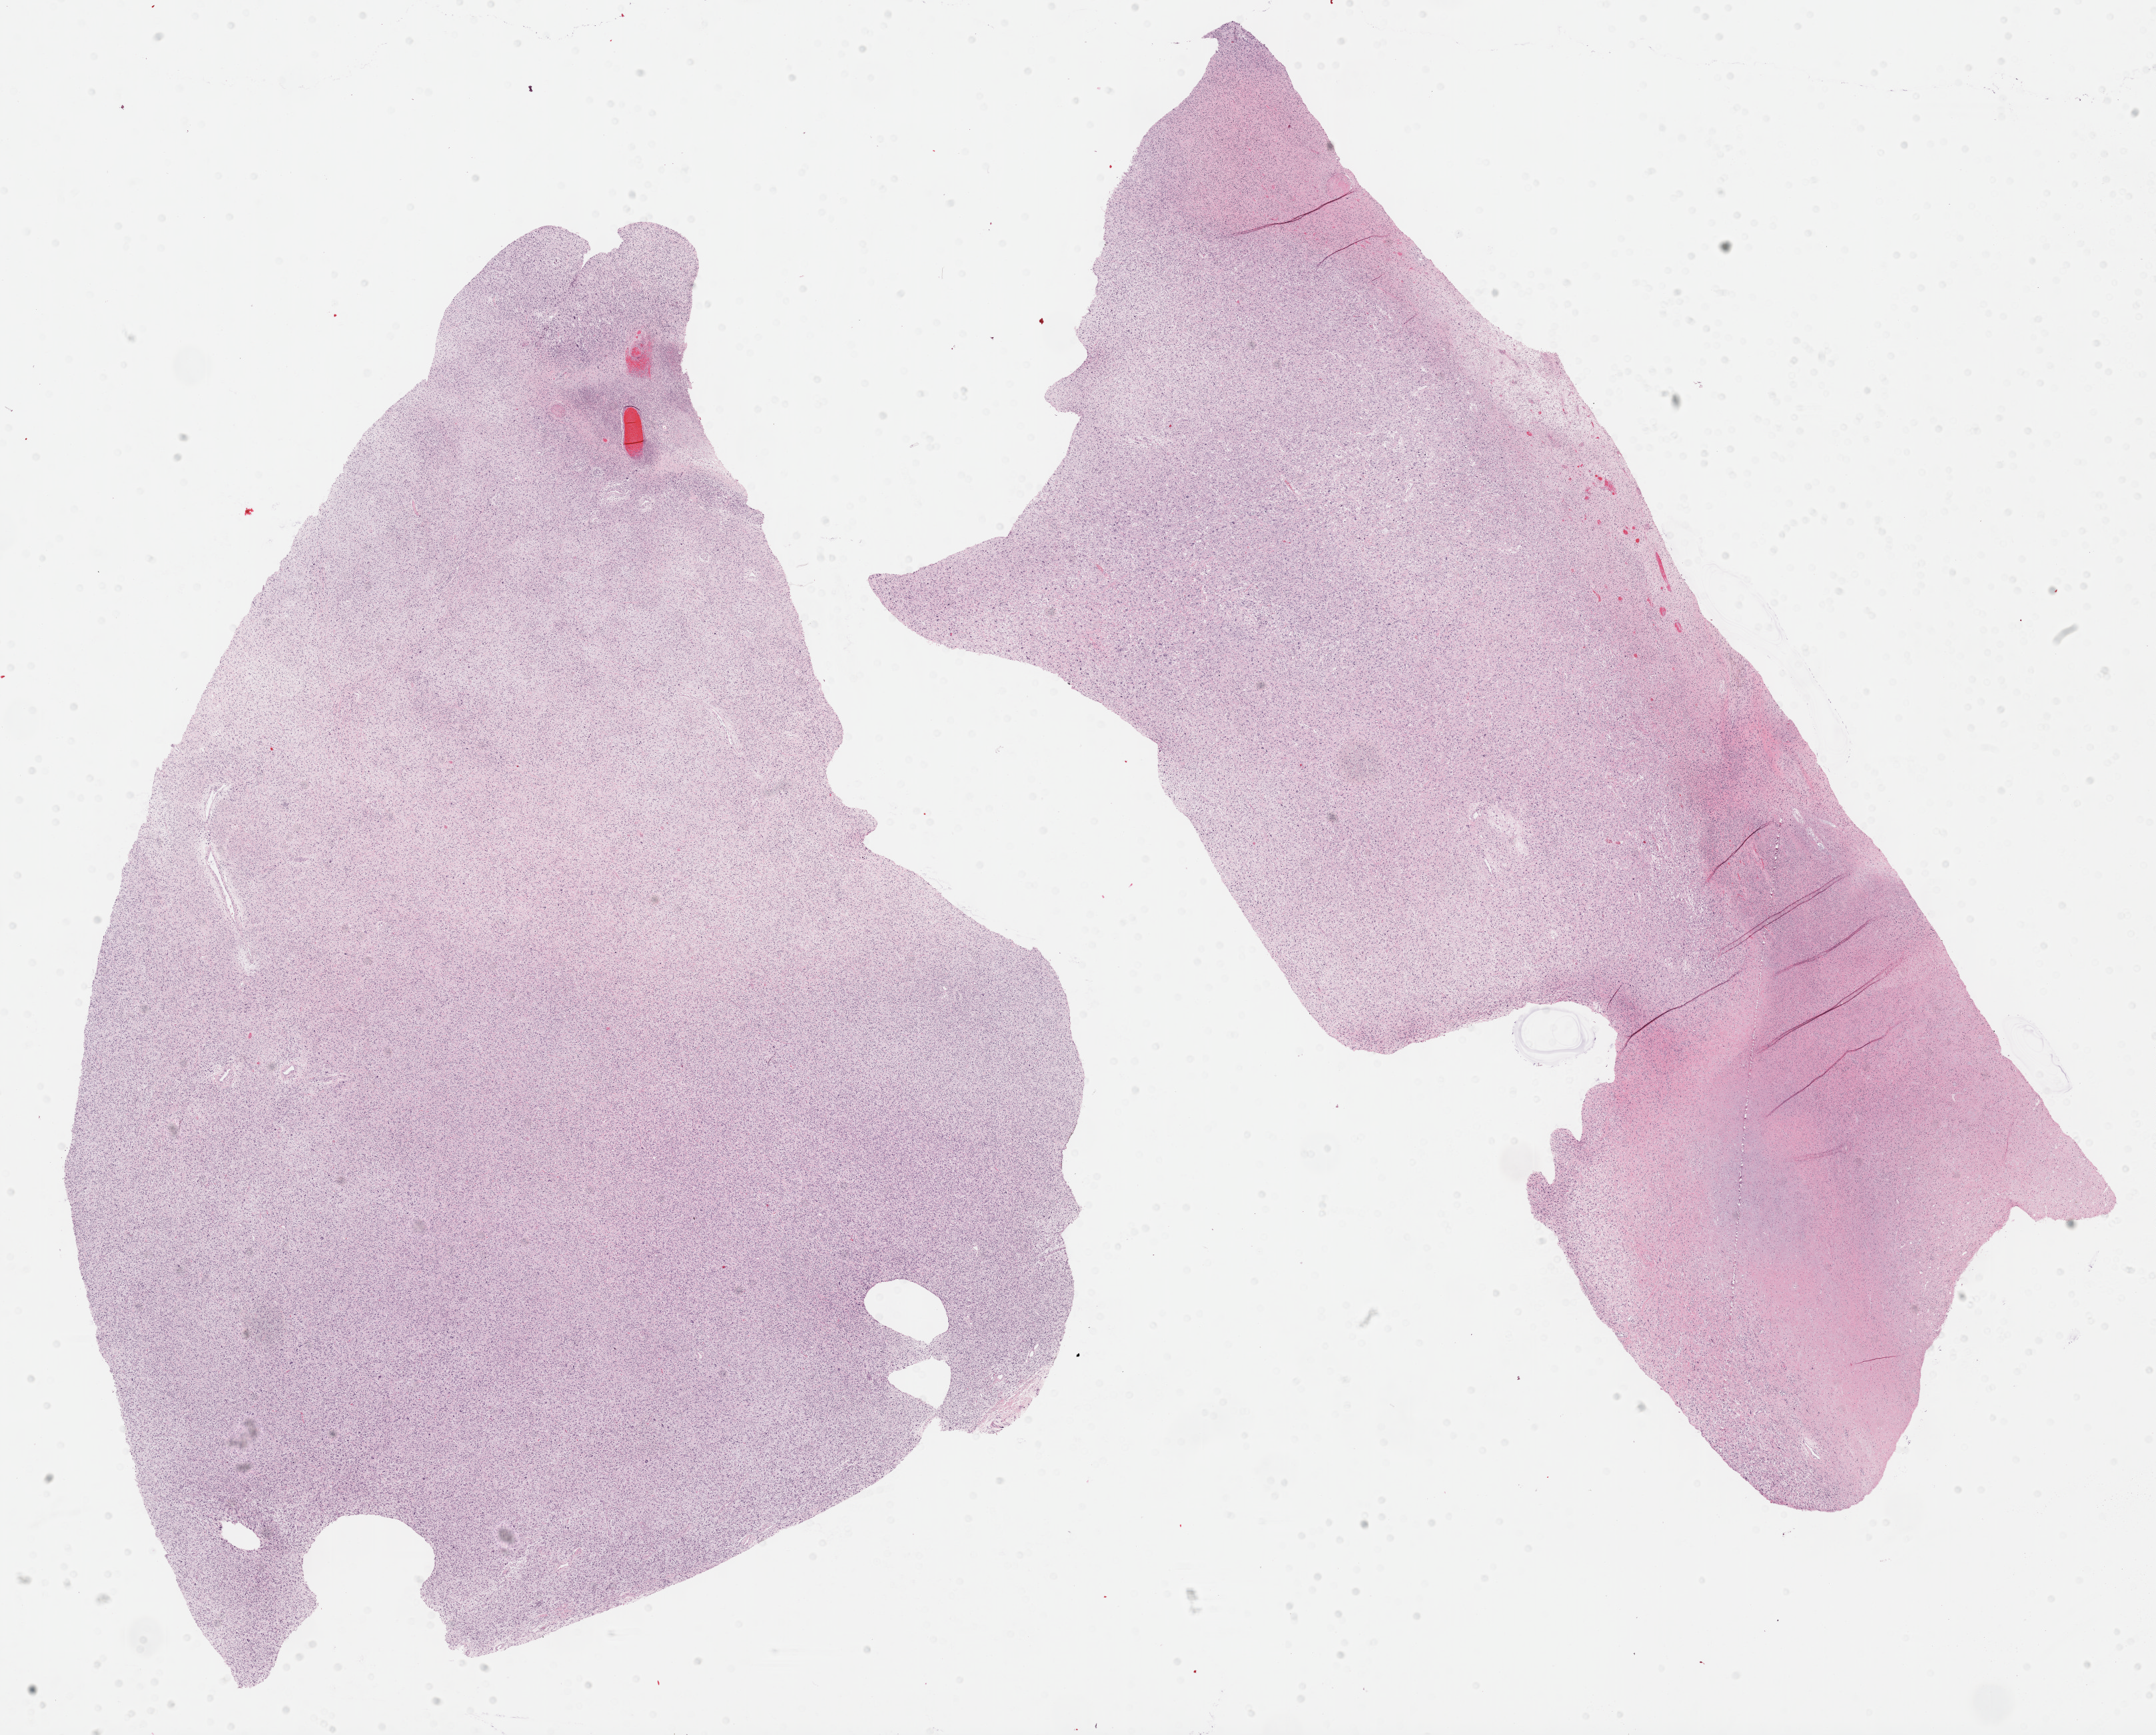
Digitized Hematoxylin and eosin (H&E) stained tissue section (whole slide), whole scanned area (about 26.2 x 21.1 mm, from a 40x scan) shown as a low-resolution overview, FFPE section, sample: primary tumour, retroperitoneum and peritoneum. Patient: female, age at initial diagnosis 76 years.
Pathologic diagnosis: Dedifferentiated liposarcoma (retroperitoneum).